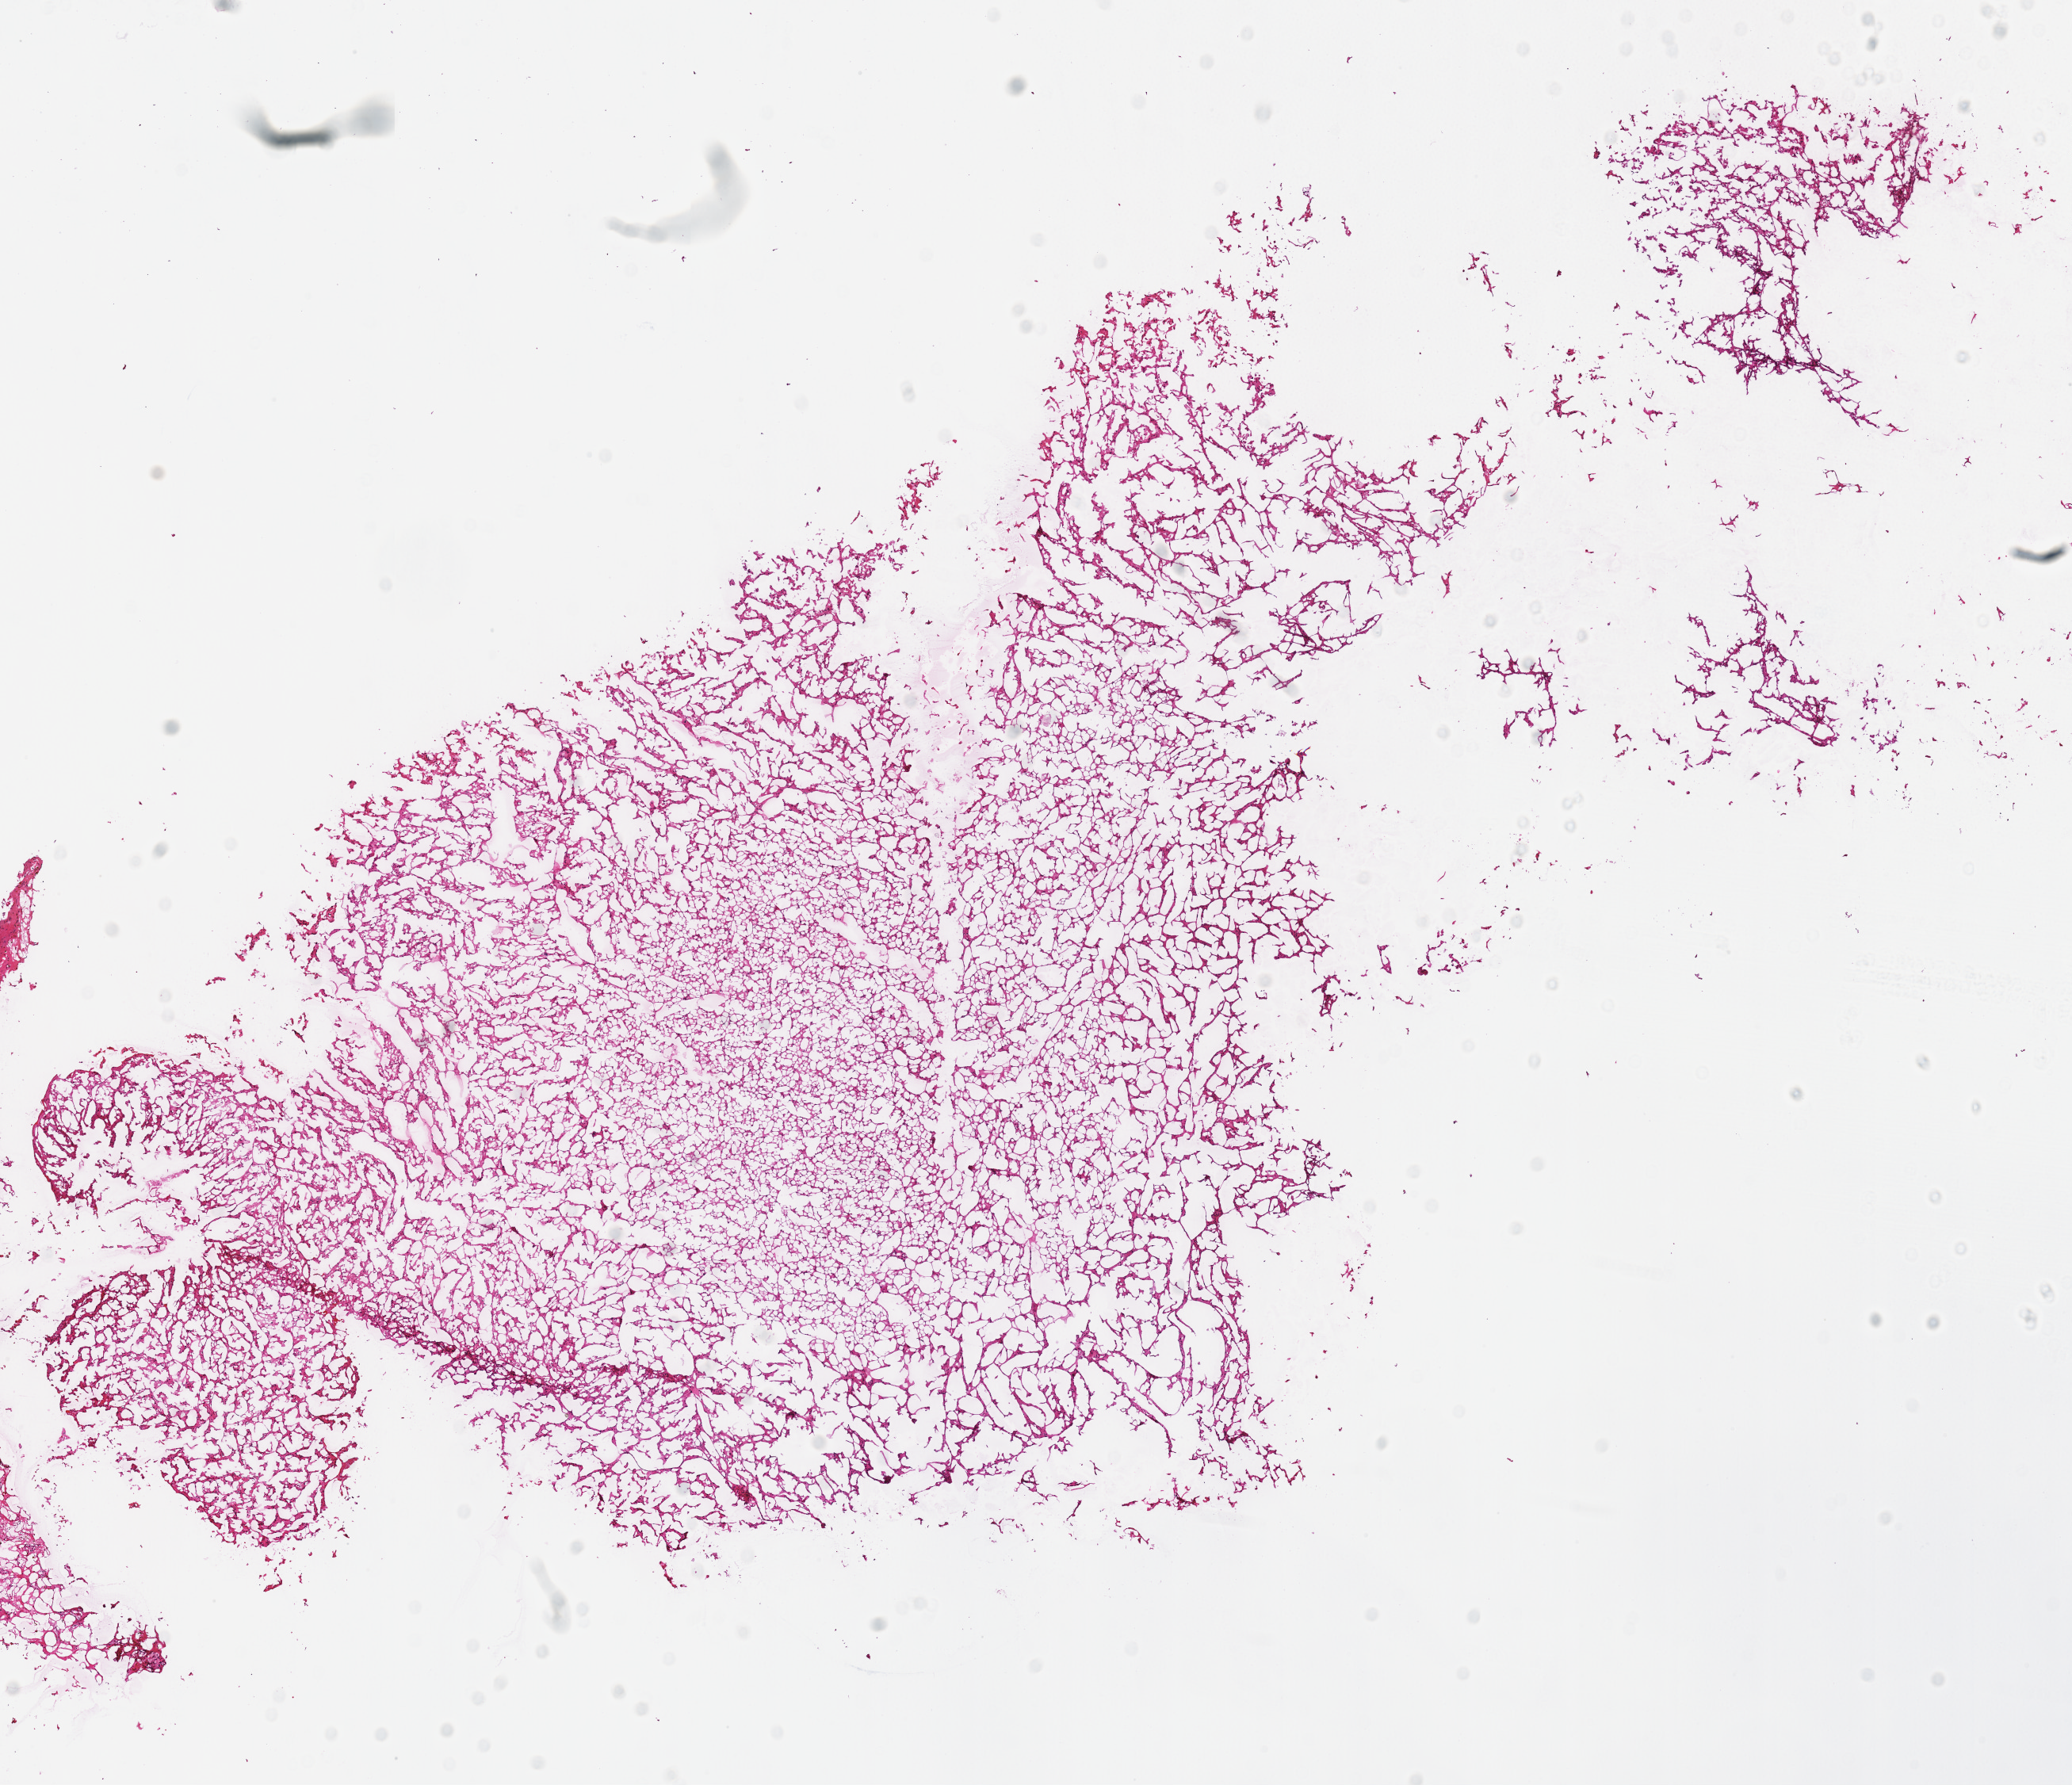
Whole-slide histology image, H&E-stained, shown as a low-resolution overview of the whole scanned area (about 10.3 x 8.9 mm); frozen section from the top of the tissue portion; primary tumour sample from the kidney. Patient: male, age at initial diagnosis 46 years.
Histologic diagnosis: Renal cell carcinoma, chromophobe type.